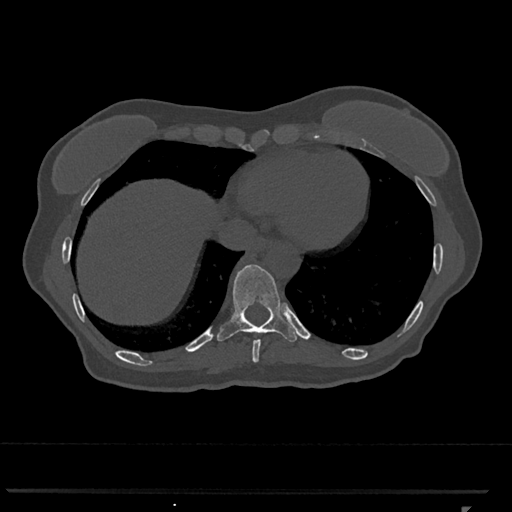
CT including the spine, one axial slice; reconstruction kernel Br40s/3; bone window (W 1800 / L 400 HU); 0.5 mm slice thickness; 512 × 512 image matrix. Patient: female, 62 years. Case-level facts recorded for this patient, not image findings: primary cancer: renal.
Outlined on this slice (semi-automatic segmentation, software-assisted and operator-edited):
- T10 vertebra: bounding box <217,264,298,342> (left, top, right, bottom; pixels)
- T9 vertebra: <252,340,261,362>